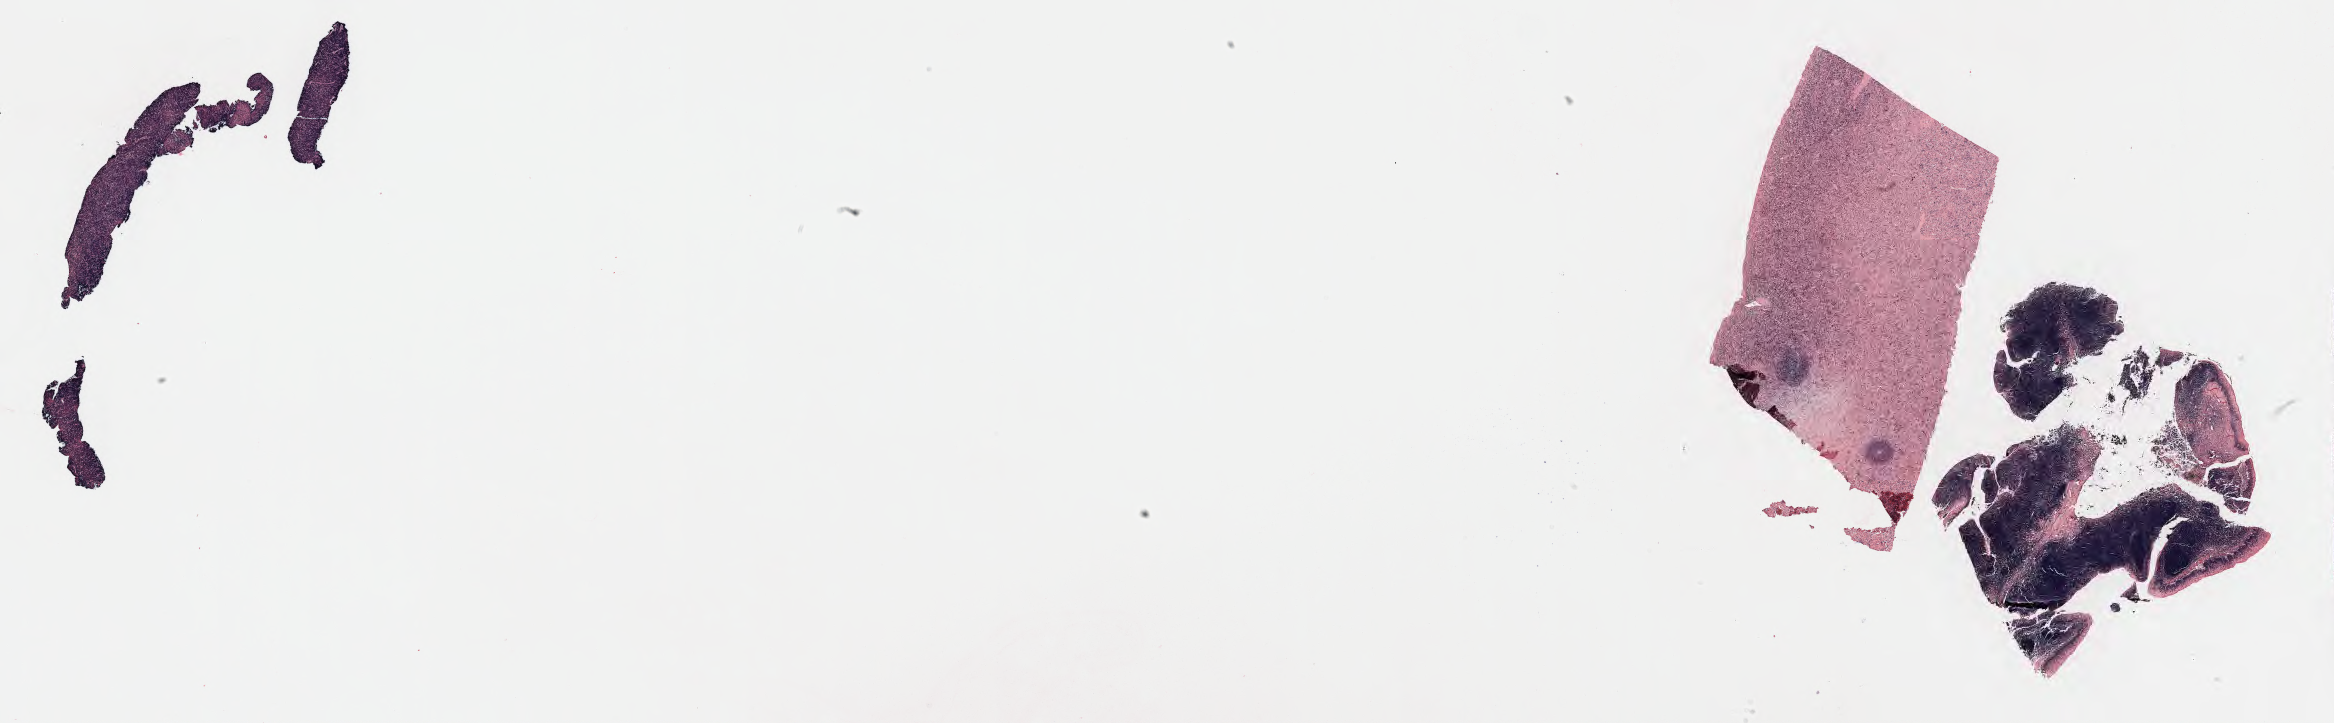
Whole-slide image; stain recorded as Iodonitrotetrazolium — whole scanned area (about 37.8 x 11.7 mm) shown as a low-resolution overview. Tumor tissue. Patient: male, aged 10.
Histologic diagnosis: Diffuse large B-cell lymphoma, NOS.